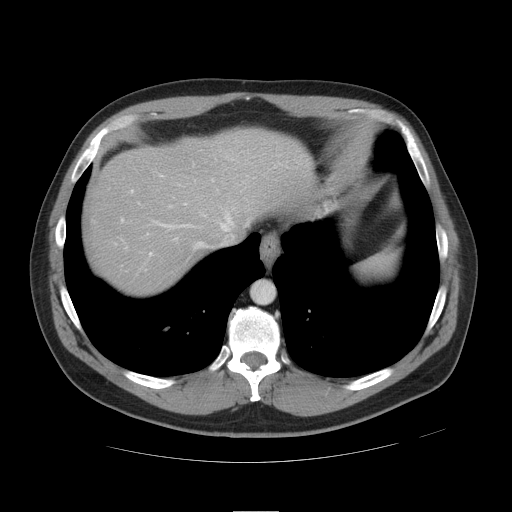
Contrast-enhanced abdominal CT, one axial slice; position 40 of 49 along the scan axis; 120 kVp; soft-tissue window (W 400 / L 40 HU); 512 × 512 image matrix, field of view 425 × 425 mm. Male patient, age 52 years. From the clinical record (not read from this slice): diagnosis: colorectal cancer liver metastases, imaged before liver resection; multiple liver metastases: yes; largest metastasis: 5.1 cm; disease in both lobes: yes.
Outlined on this slice (outlined manually by an expert reader):
- hepatic veins: bounding box (x1, y1, x2, y2) in pixels: (158, 206, 237, 248)
- liver: (90, 132, 307, 292)
- planned liver remnant (the part of the liver to remain after resection): (139, 132, 307, 231)
- portal vein (with intrahepatic branches): (121, 189, 153, 257)